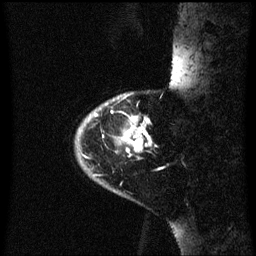
Breast MRI (dynamic contrast-enhanced), one sagittal slice. Position 10 of 60 along the scan axis. Dynamic contrast-enhanced series, image 2 of 3 at this slice position (ordered by acquisition). 1.5 T. TE 4.2 ms, TR 8.4 ms. 2.3 mm slice thickness. 256 × 256 image matrix. Patient: female, 46 years. Case-level facts recorded for this patient, not image findings: setting: breast cancer imaged before/during neoadjuvant chemotherapy; receptor status: HER2-positive.
Annotated regions visible in this slice (semi-automatic segmentation, software-assisted and operator-edited):
- analysis volume of interest (the breast-tissue region the enhancement analysis was run in; not a lesion): bounding box (x1, y1, x2, y2) in pixels: (76, 86, 173, 171)
- tumour enhancement mask (voxels above the 70 % enhancement threshold inside the analysis volume of interest): (122, 118, 149, 153)